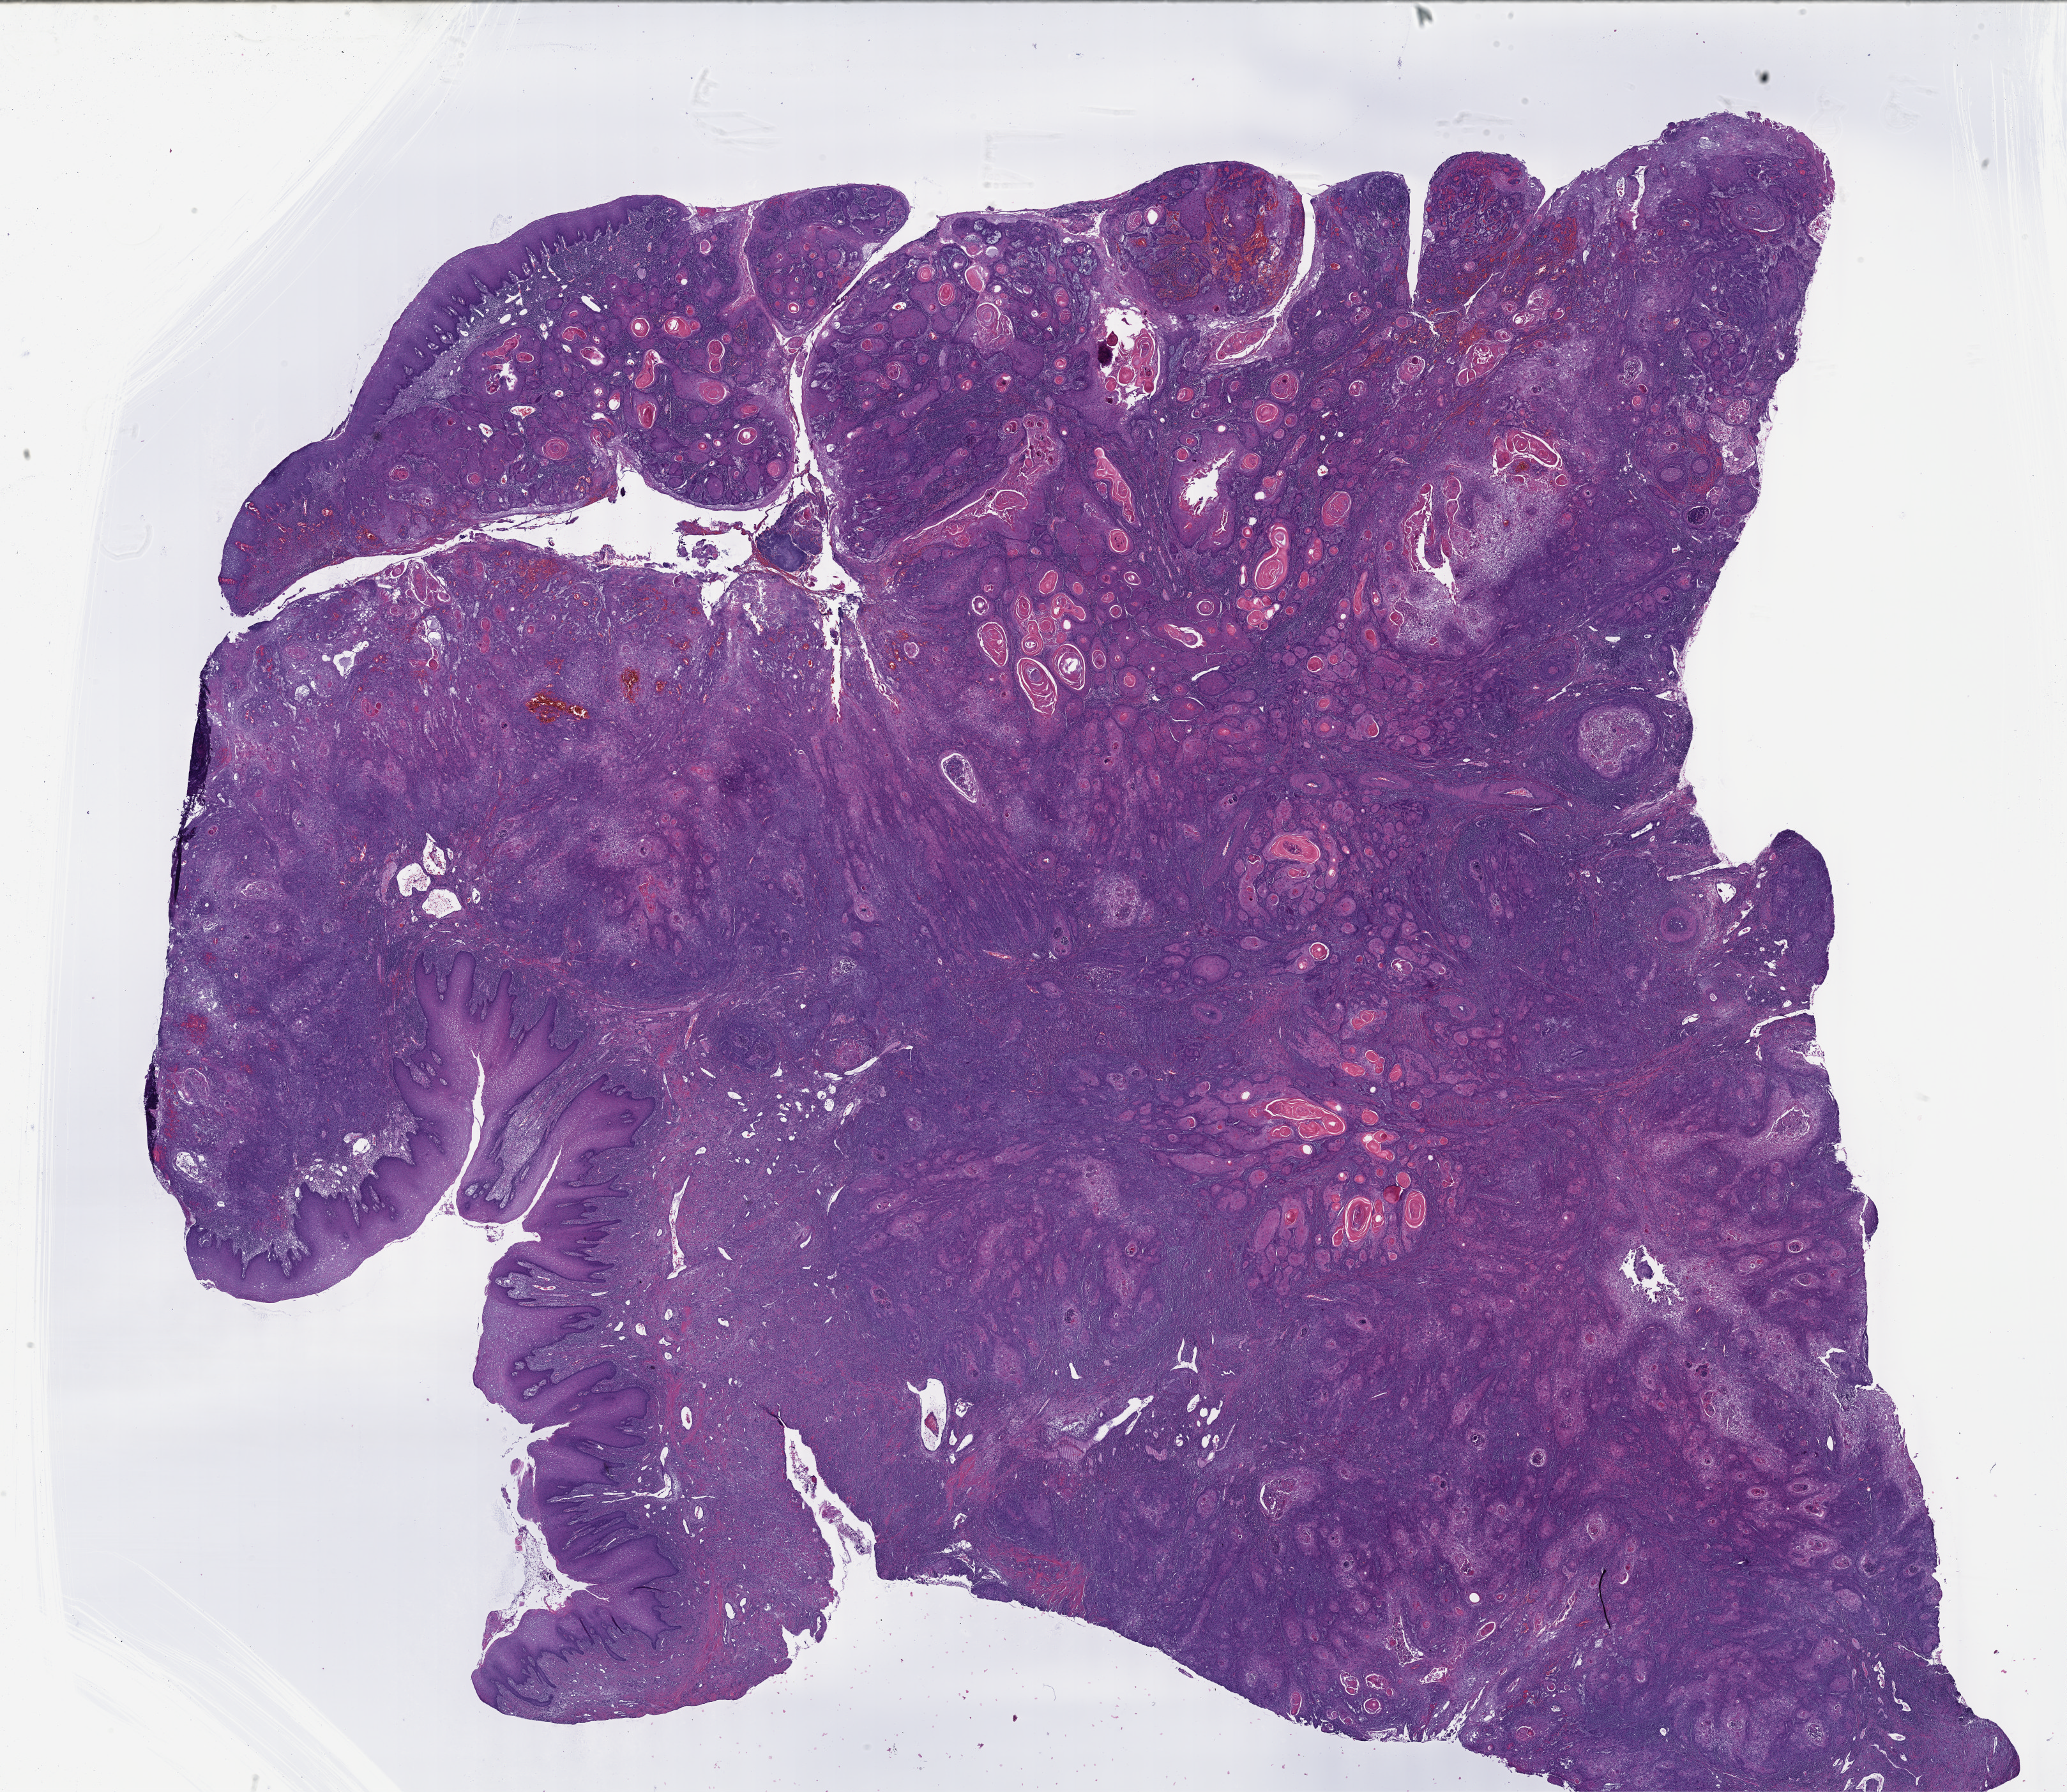
H&E-stained whole-slide image, a low-resolution overview of the entire scanned area, about 26.2 x 22.7 mm (from a 40x scan), formalin-fixed paraffin-embedded (FFPE) diagnostic section, primary tumour sample from the head and neck. Female, age 62 years at initial diagnosis. Histologic grade: G3 (poorly differentiated).
• diagnosis: Squamous cell carcinoma, NOS (tongue, NOS)
• AJCC pathologic stage: III (7th edition)
• lymph nodes positive (case pathology): 1 of 58 examined